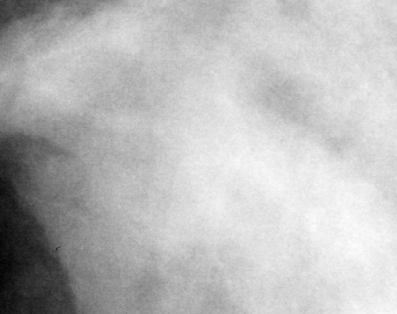
Crop from a digitized film mammogram around one marked abnormality, right breast, CC view.
Mass, shape oval, margins circumscribed; BI-RADS assessment category 3; pathology result (as recorded, not read from the image): benign.